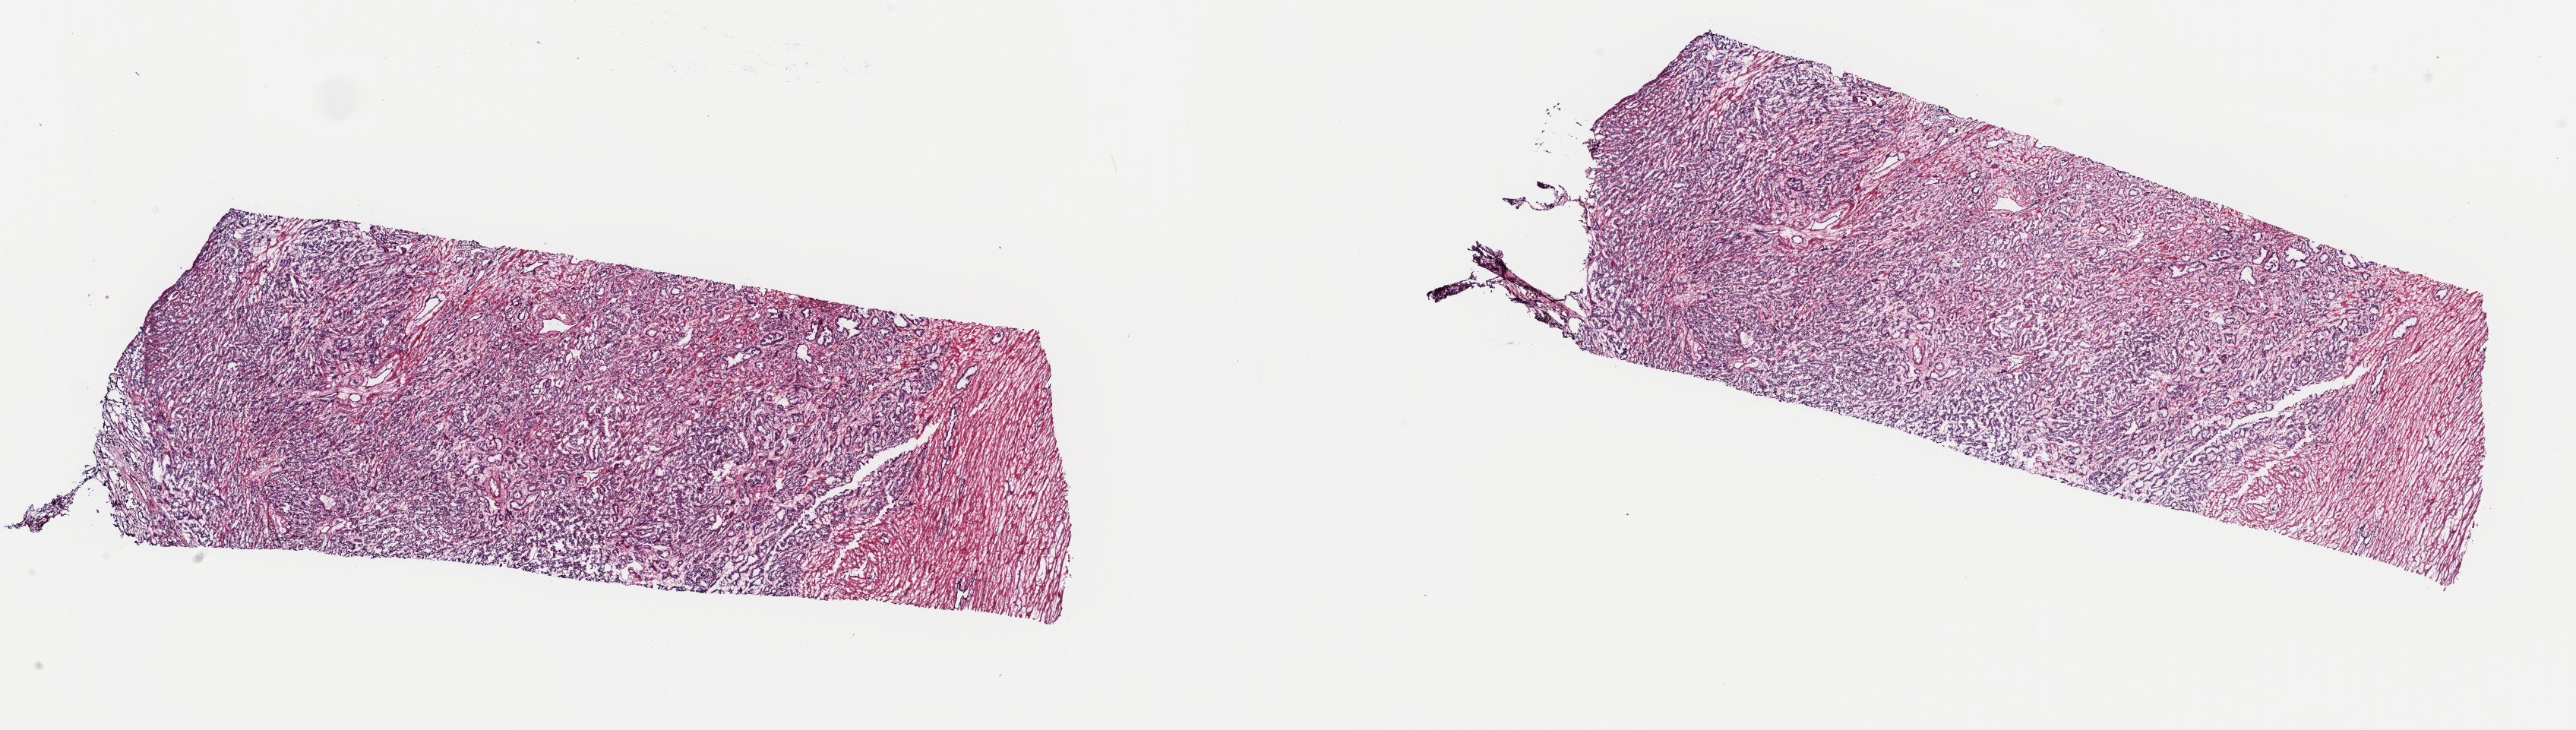
Digitized Hematoxylin and eosin (H&E) stained tissue section (whole slide), low-resolution overview of the scanned area, about 26.8 x 7.6 mm (acquisition: 40x scan); frozen section from the top of the tissue portion; prostate, primary tumour sample. Patient: male, age at initial diagnosis 58 years.
Diagnosis: Acinar cell carcinoma (prostate gland).